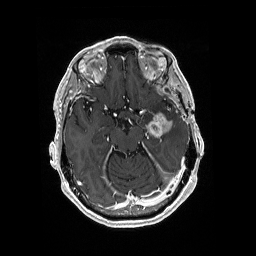
Brain MRI from a brain-tumour surgery series, one axial slice; T1-weighted post-contrast; 1 mm slice thickness; 256 × 256 image matrix, field of view 256 × 256 mm. Case-level facts recorded for this patient, not image findings: histopathology: Glioblastoma; WHO grade: 4; IDH mutation: no.
Annotated regions visible in this slice (outlined manually by an expert reader):
- tumour: bounding box (x1, y1, x2, y2) in pixels: (146, 111, 174, 137)